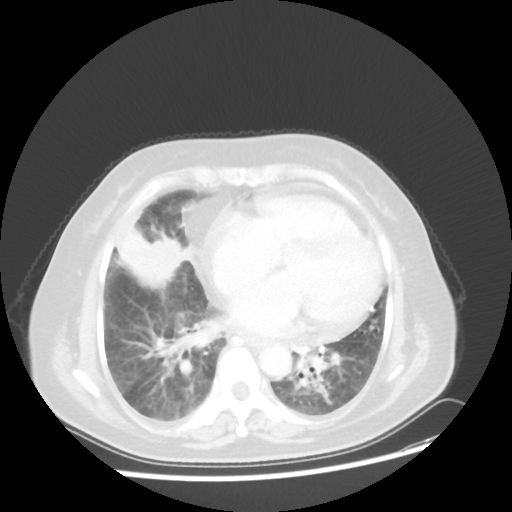
Chest CT, one axial slice. Position 18 of 45 along the scan axis. Reconstruction kernel STANDARD. Lung window (W 1500 / L -600 HU). 5 mm slice thickness. 512 × 512 image matrix, field of view 359 × 359 mm. Female patient, age 67 years. Case-level facts recorded for this patient, not image findings: clinical TNM (as recorded): T2a N3 M1a.
Outlined on this slice (bounding box drawn by a radiologist):
- lung tumour (recorded histology: adenocarcinoma): bounding box [x1, y1, x2, y2] px = [117, 223, 184, 289]